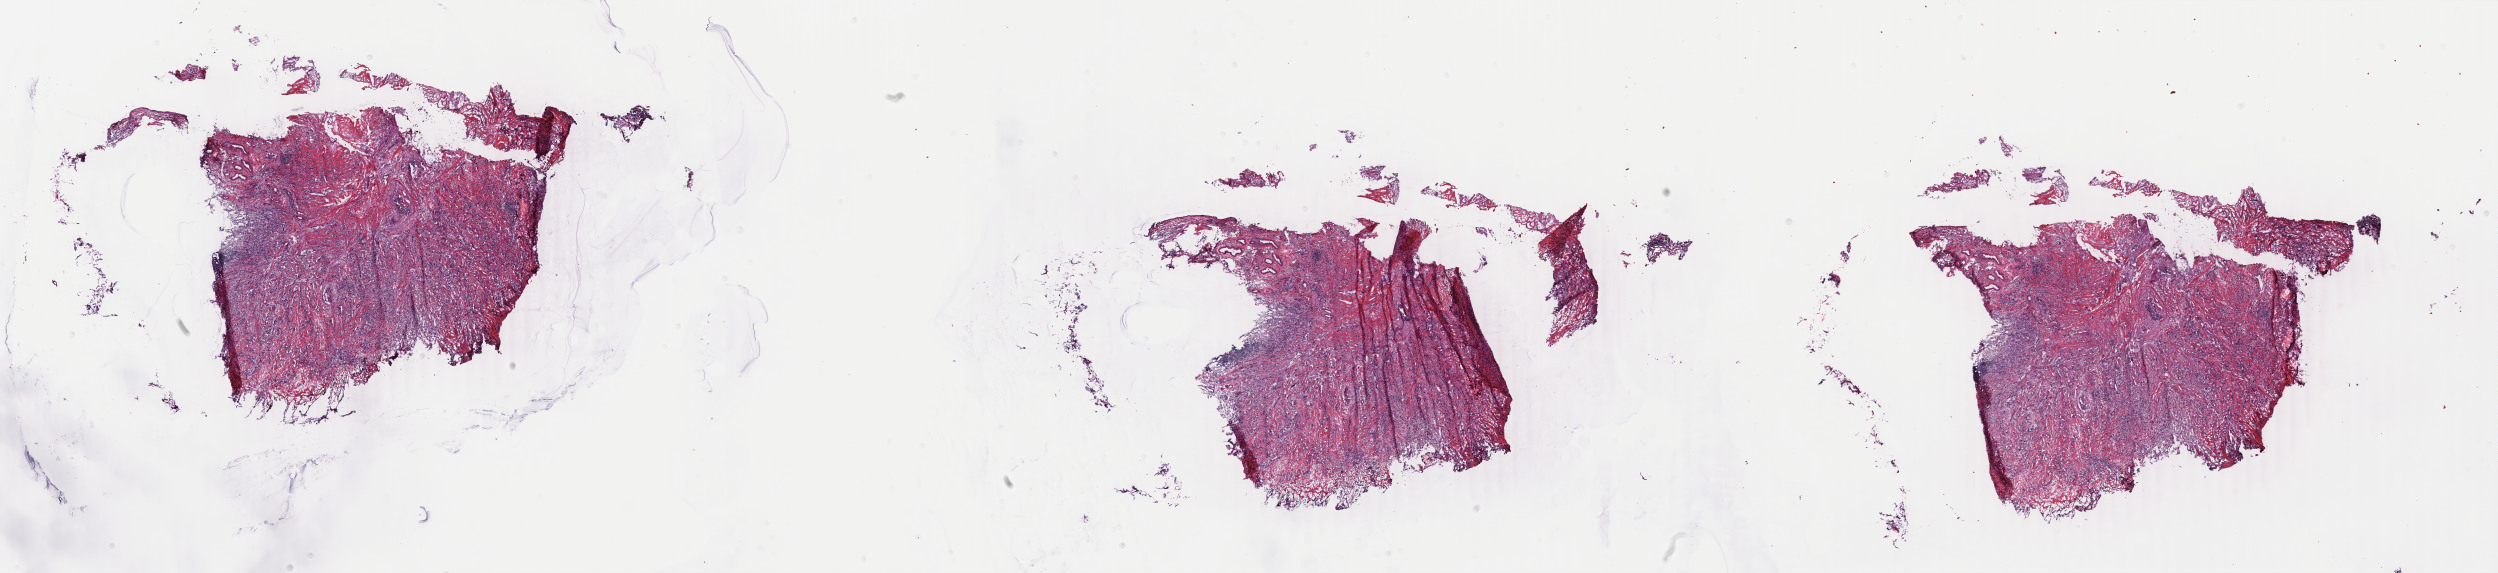
Digitized H&E-stained tissue section (whole slide), low-resolution overview of the scanned area, about 39.7 x 9.1 mm (from a 40x scan); frozen section; breast, primary tumour sample. Female, age 61 years at initial diagnosis. Pathologist review of this section (percent, as recorded): tumour cells 75%, tumour nuclei 75%, normal cells 1%, stromal cells 24%, necrosis 0%. Inflammatory infiltration, as recorded: lymphocyte infiltration 1%, monocyte infiltration 0%, neutrophil infiltration 0%.
Lymph nodes positive (case pathology): 0 of 10 examined. Laterality: right. AJCC pathologic stage: IA (7th edition). Diagnosis: Infiltrating duct carcinoma, NOS. TNM: T1c N0 M0.